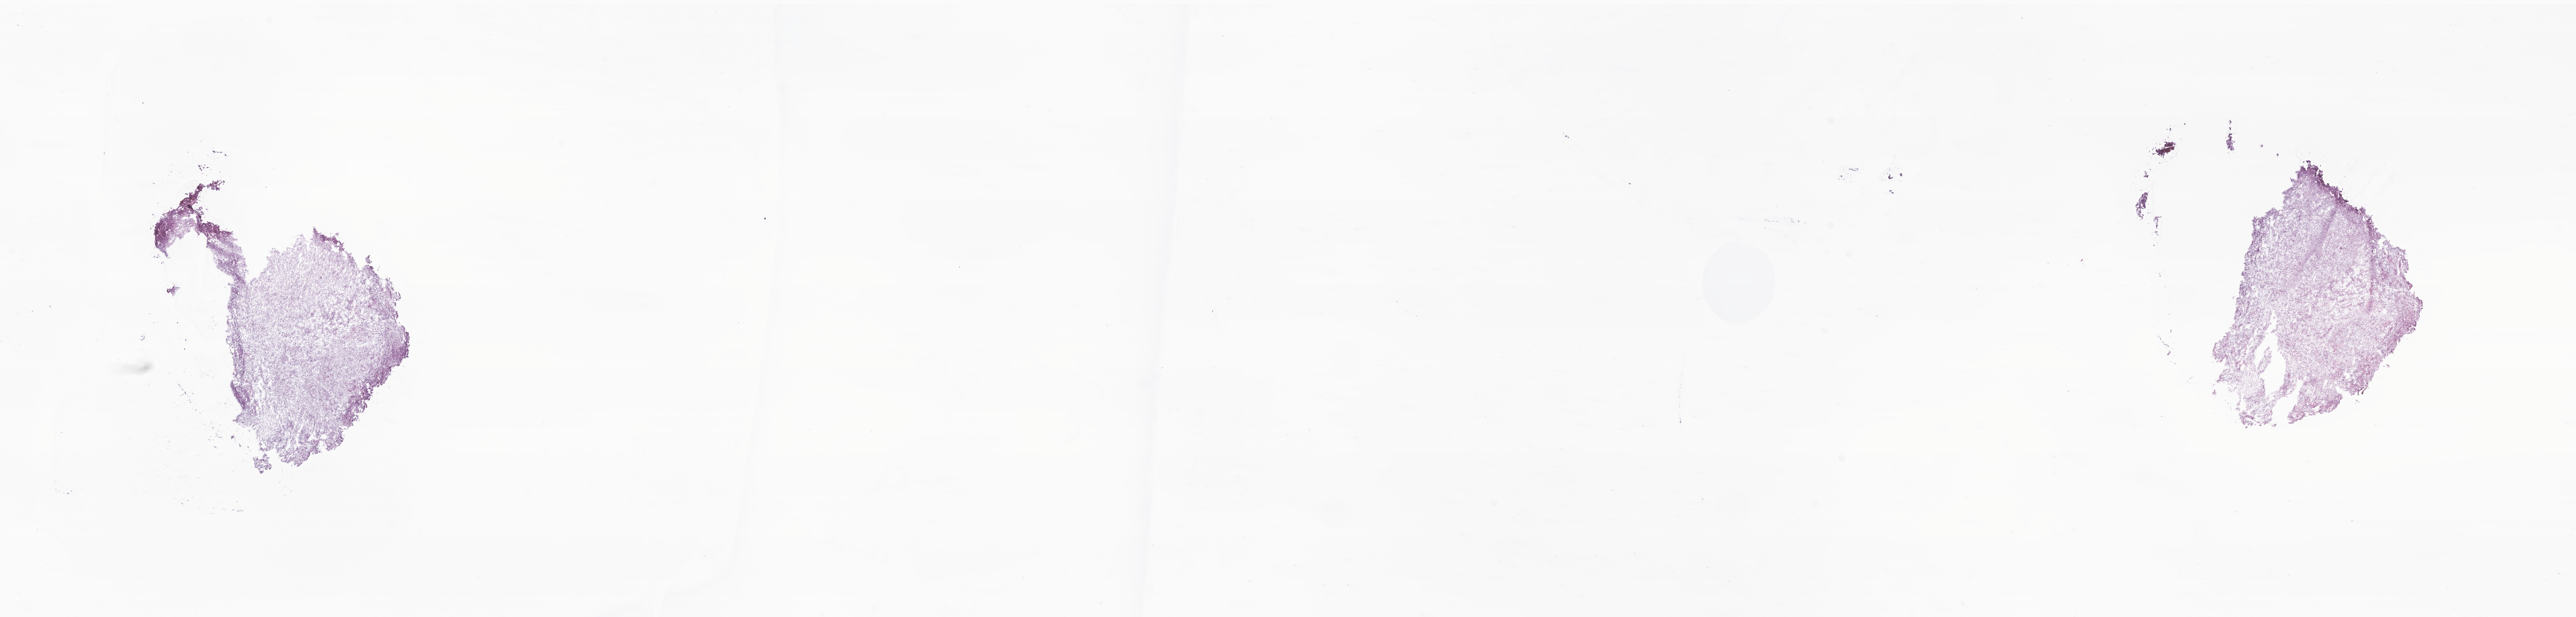
Haematoxylin and eosin whole-slide image of tumor tissue from the brain — low-resolution overview of the scanned area, about 32.7 x 7.8 mm; frozen section. Male patient, age 39 months (3 years 3 months).
Diagnosis (ICD-O-3 morphology term): Pilocytic astrocytoma.